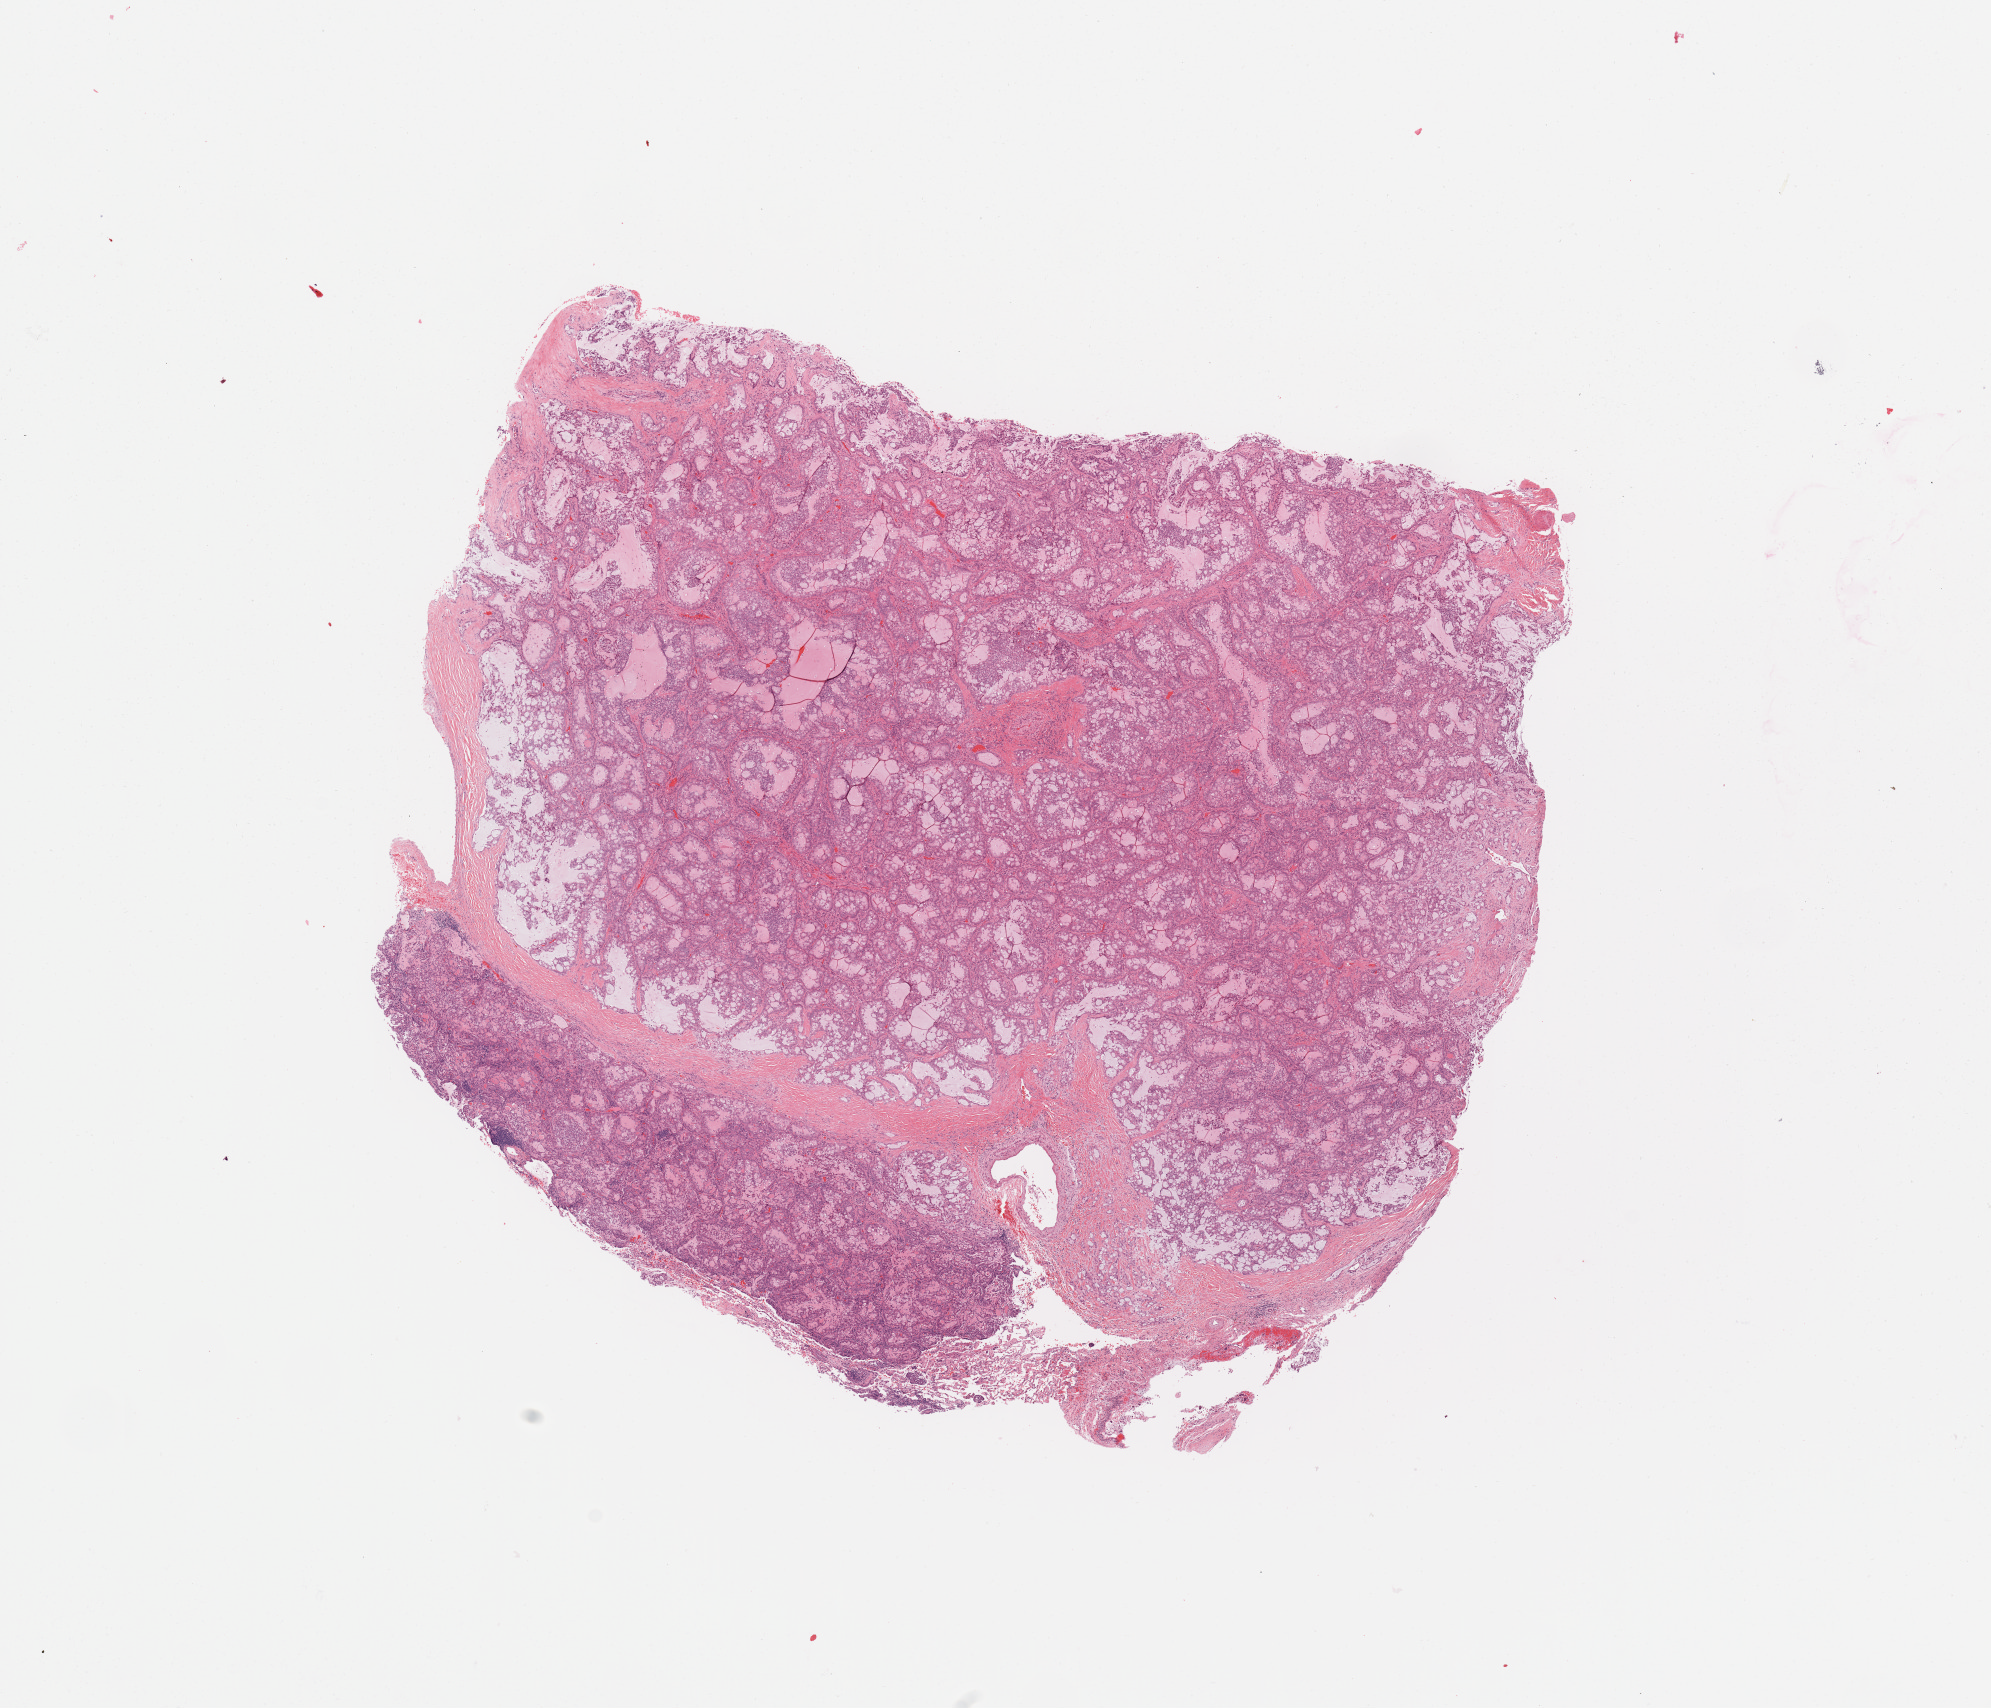
H&E whole-slide image — whole scanned area (about 15.8 x 13.5 mm, from a 20x scan) shown as a low-resolution overview, tumour tissue sample, sampled site: lung. 59-year-old female patient. Histologic grade: G2 (moderately differentiated). Pathologist review of this section (percent, as recorded): tumour nuclei 80%, necrosis 0%.
• primary tumour site (as recorded): left lower lobe
• AJCC pathologic stage: IA
• histologic diagnosis: Adenocarcinoma, NOS